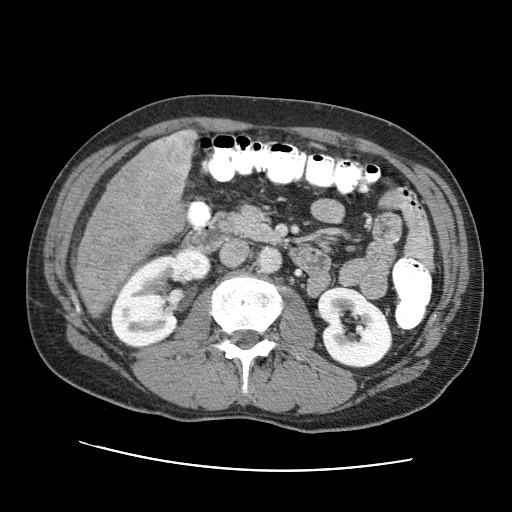
Contrast-enhanced abdominal CT (liver protocol), one axial slice; slice 22 of 95 in the series (ordered by position); reconstruction kernel STANDARD; 120 kVp; one of 2 acquisitions stored at this slice position; soft-tissue window (W 400 / L 40 HU); 2.5 mm slice thickness; 512 × 512 image matrix, field of view 360 × 360 mm. From the clinical record (not read from this slice): diagnosis: hepatocellular carcinoma (patient treated with transarterial chemoembolisation; whether this scan precedes or follows treatment is not stated here); TNM stage (as recorded): Stage-IVA.
Structures marked on this image (semi-automatic segmentation, software-assisted and operator-edited):
- liver parenchyma outside the tumour (the mass and vessels are separate outlines, so this box may not span the whole liver): bounding box (x1, y1, x2, y2) in pixels: (74, 130, 196, 268)
- mass: (74, 129, 195, 319)